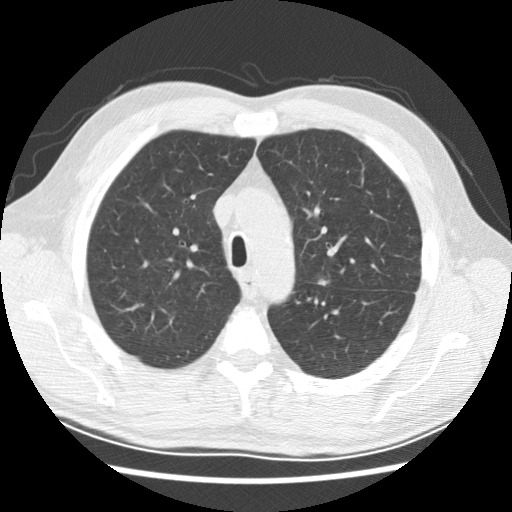
Axial slice from a low-dose chest CT screening exam; baseline annual screen; lung window (W 1500 / L -600 HU); 2.5 mm slice thickness; standard (soft-tissue) reconstruction kernel (STANDARD); 512 × 512 image matrix. Male participant, aged 59 years at enrolment. Current smoker at enrolment.
Expert reader's lesion annotation, bounding box (x1, y1, x2, y2) in pixels: (302, 268, 342, 295). Screening reader's record for this exam (one nodule recorded; not confirmed to be the boxed lesion): non-calcified nodule or mass ≥4 mm, left upper lobe, 8 × 5 mm, smooth margins, soft tissue attenuation. Official screen result: positive, change unspecified: nodule(s) >= 4 mm or enlarging nodule(s), mass(es), or other non-specific abnormalities suspicious for lung cancer. Participant outcome: lung cancer diagnosed 645 days after this screen (after the second annual screen) — adenocarcinoma, NOS, left upper lobe, left lower lobe, poorly differentiated (G3), stage IV (AJCC 6th edition).